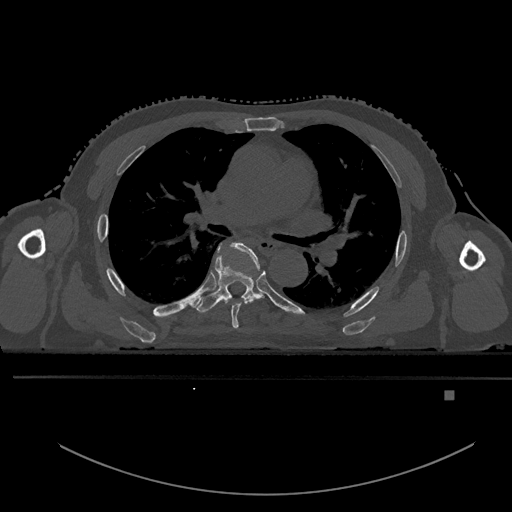
CT including the spine, one axial slice; slice 330 of 969 in the series (ordered by position); bone window (W 1800 / L 400 HU); 512 × 512 image matrix, field of view 456 × 456 mm. Patient: male, 82 years. Case-level facts recorded for this patient, not image findings: primary cancer: prostate; vertebrae with lytic lesions (as recorded): T11, T9, T8, T2.
Structures marked on this image (semi-automatically segmented with operator editing):
- T5 vertebra: bounding box [x1, y1, x2, y2] px = [223, 242, 261, 329]
- T6 vertebra: [191, 242, 261, 313]